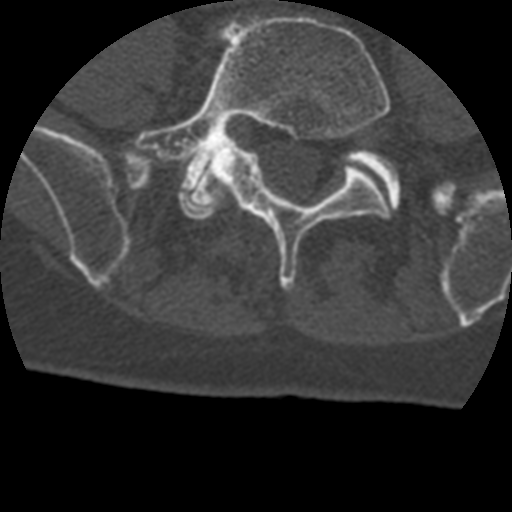
CT including the spine, one axial slice. Bone window (W 1800 / L 400 HU). 1.25 mm slice thickness. 512 × 512 image matrix. Patient age 69 years. Case-level facts recorded for this patient, not image findings: primary cancer: prostate.
Outlined on this slice (semi-automatic segmentation, software-assisted and operator-edited):
- L4 vertebra: bounding box [x1, y1, x2, y2] px = [212, 187, 232, 207]
- L5 vertebra: [132, 15, 391, 291]